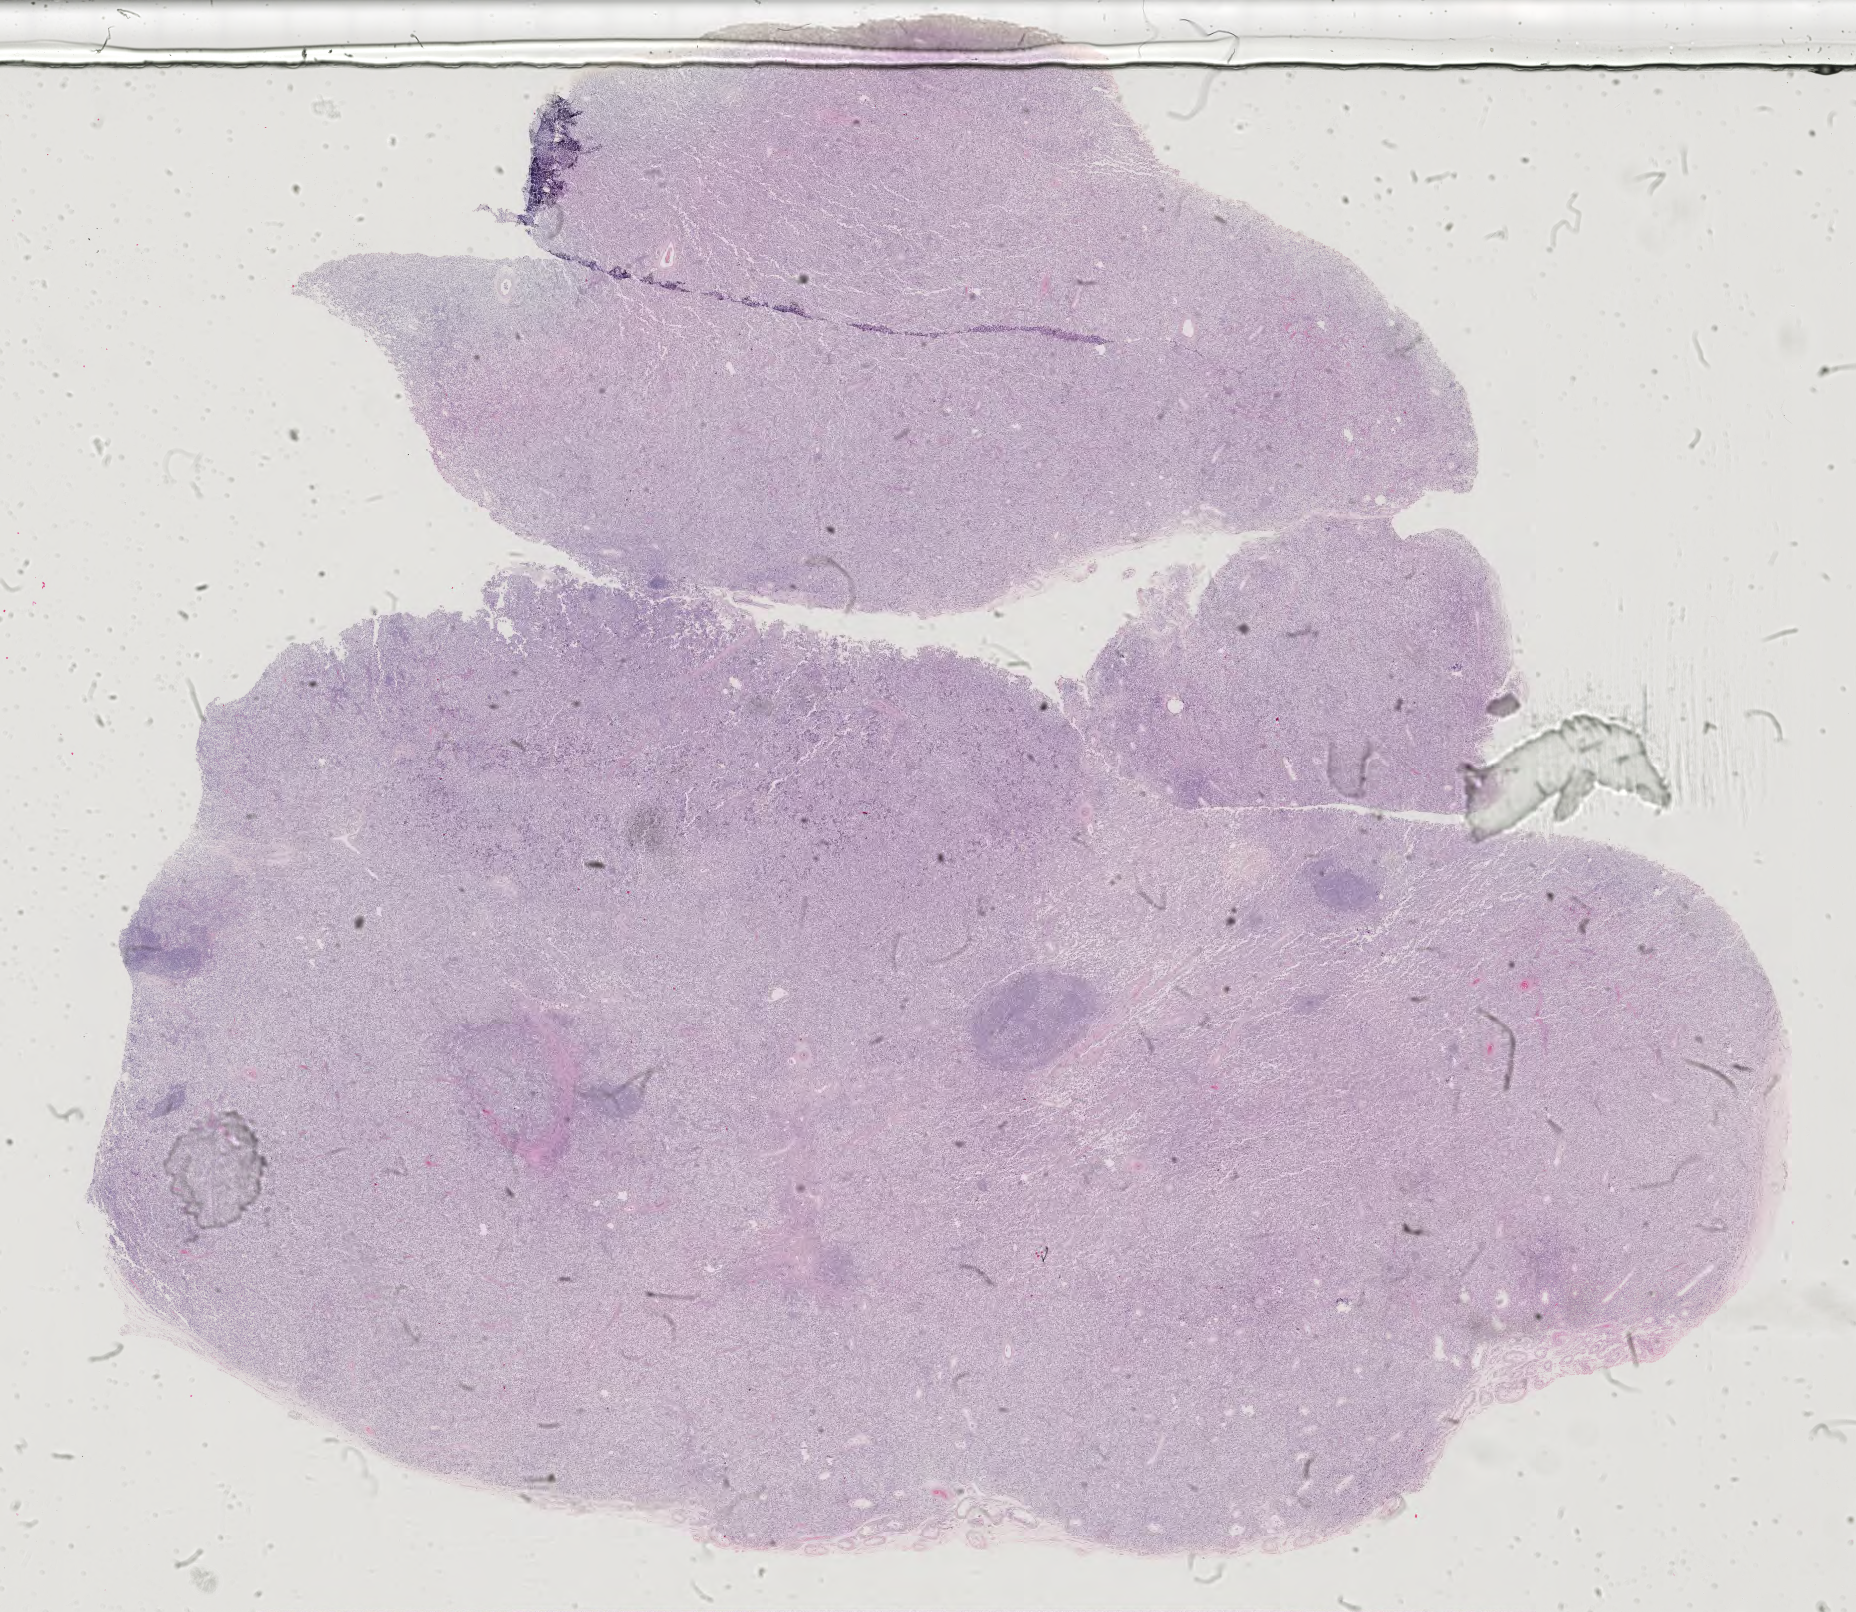
Digitized H&E tissue section (whole slide), whole scanned area (about 27.0 x 23.5 mm, acquisition: 40x scan) shown as a low-resolution overview. FFPE section. Testis, primary tumour sample. Patient: male, age at initial diagnosis 30 years.
* diagnosis: Seminoma, NOS
* AJCC pathologic stage: I (6th edition)
* TNM: T1 N0 M0